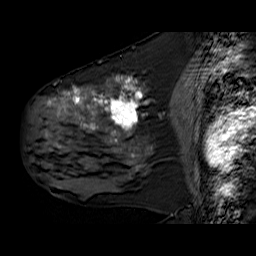
Breast MRI (dynamic contrast-enhanced), one sagittal slice. Slice 32 of 60 in the series (ordered by position). Dynamic contrast-enhanced series, time point 2 of 6 at this slice position (early post-contrast). 1.5 T. TE 6.3 ms, TR 32.9 ms. 4 mm slice thickness. 256 × 256 image matrix, field of view 200 × 200 mm. Female patient. Case-level facts recorded for this patient, not image findings: setting: breast cancer imaged before/during neoadjuvant chemotherapy; receptor status: HER2-positive.
Outlined on this slice (semi-automatic segmentation, software-assisted and operator-edited):
- analysis volume of interest (the breast-tissue region the enhancement analysis was run in; not a lesion): bounding box (x1, y1, x2, y2) in pixels: (30, 78, 171, 180)
- tumour enhancement mask (voxels above the 100 % enhancement threshold inside the analysis volume of interest): (48, 78, 146, 142)